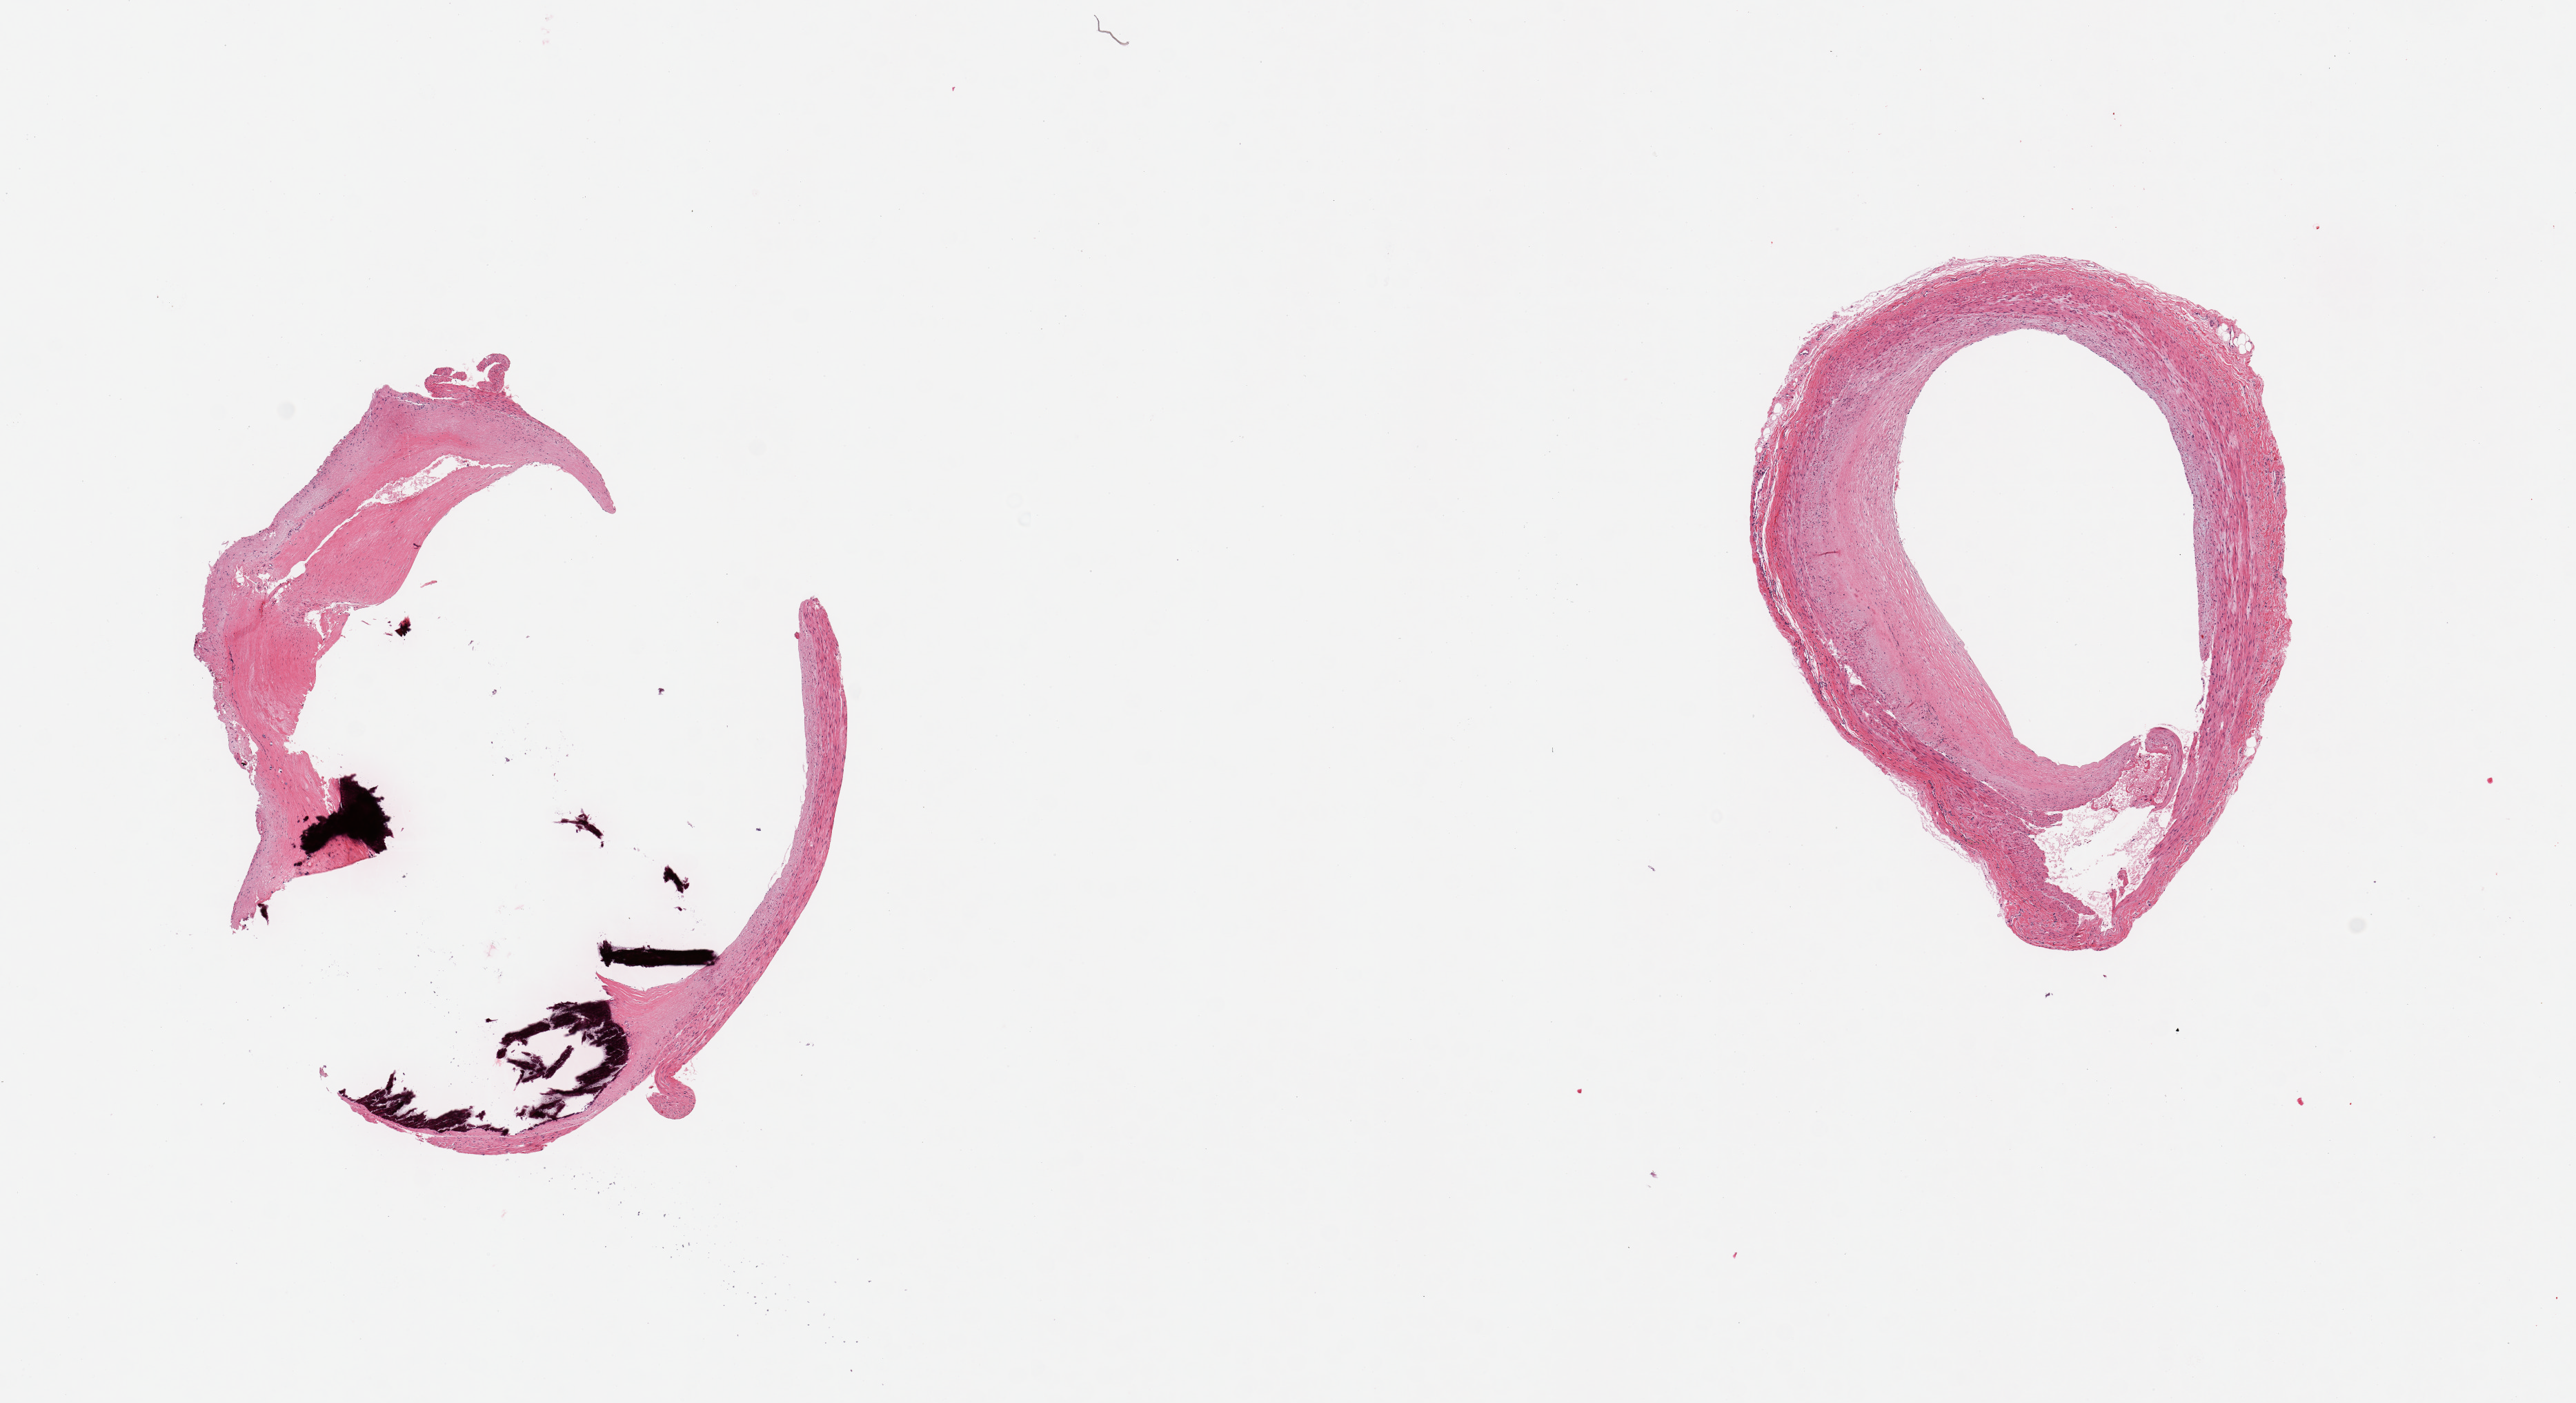
Haematoxylin and eosin whole-slide image, brightfield, shown as a low-resolution overview of the whole scanned area (about 14.8 x 8.0 mm, acquisition: 20x scan). PAXgene-fixed paraffin-embedded (PFPE) section. Sampled site (target tissue): coronary artery. Tissue donor sample.
* pathologist's review note for this sample: 2 pieces, 1 fragmented with large eccentric calcified plaque; other with moderate atheromatous plaque